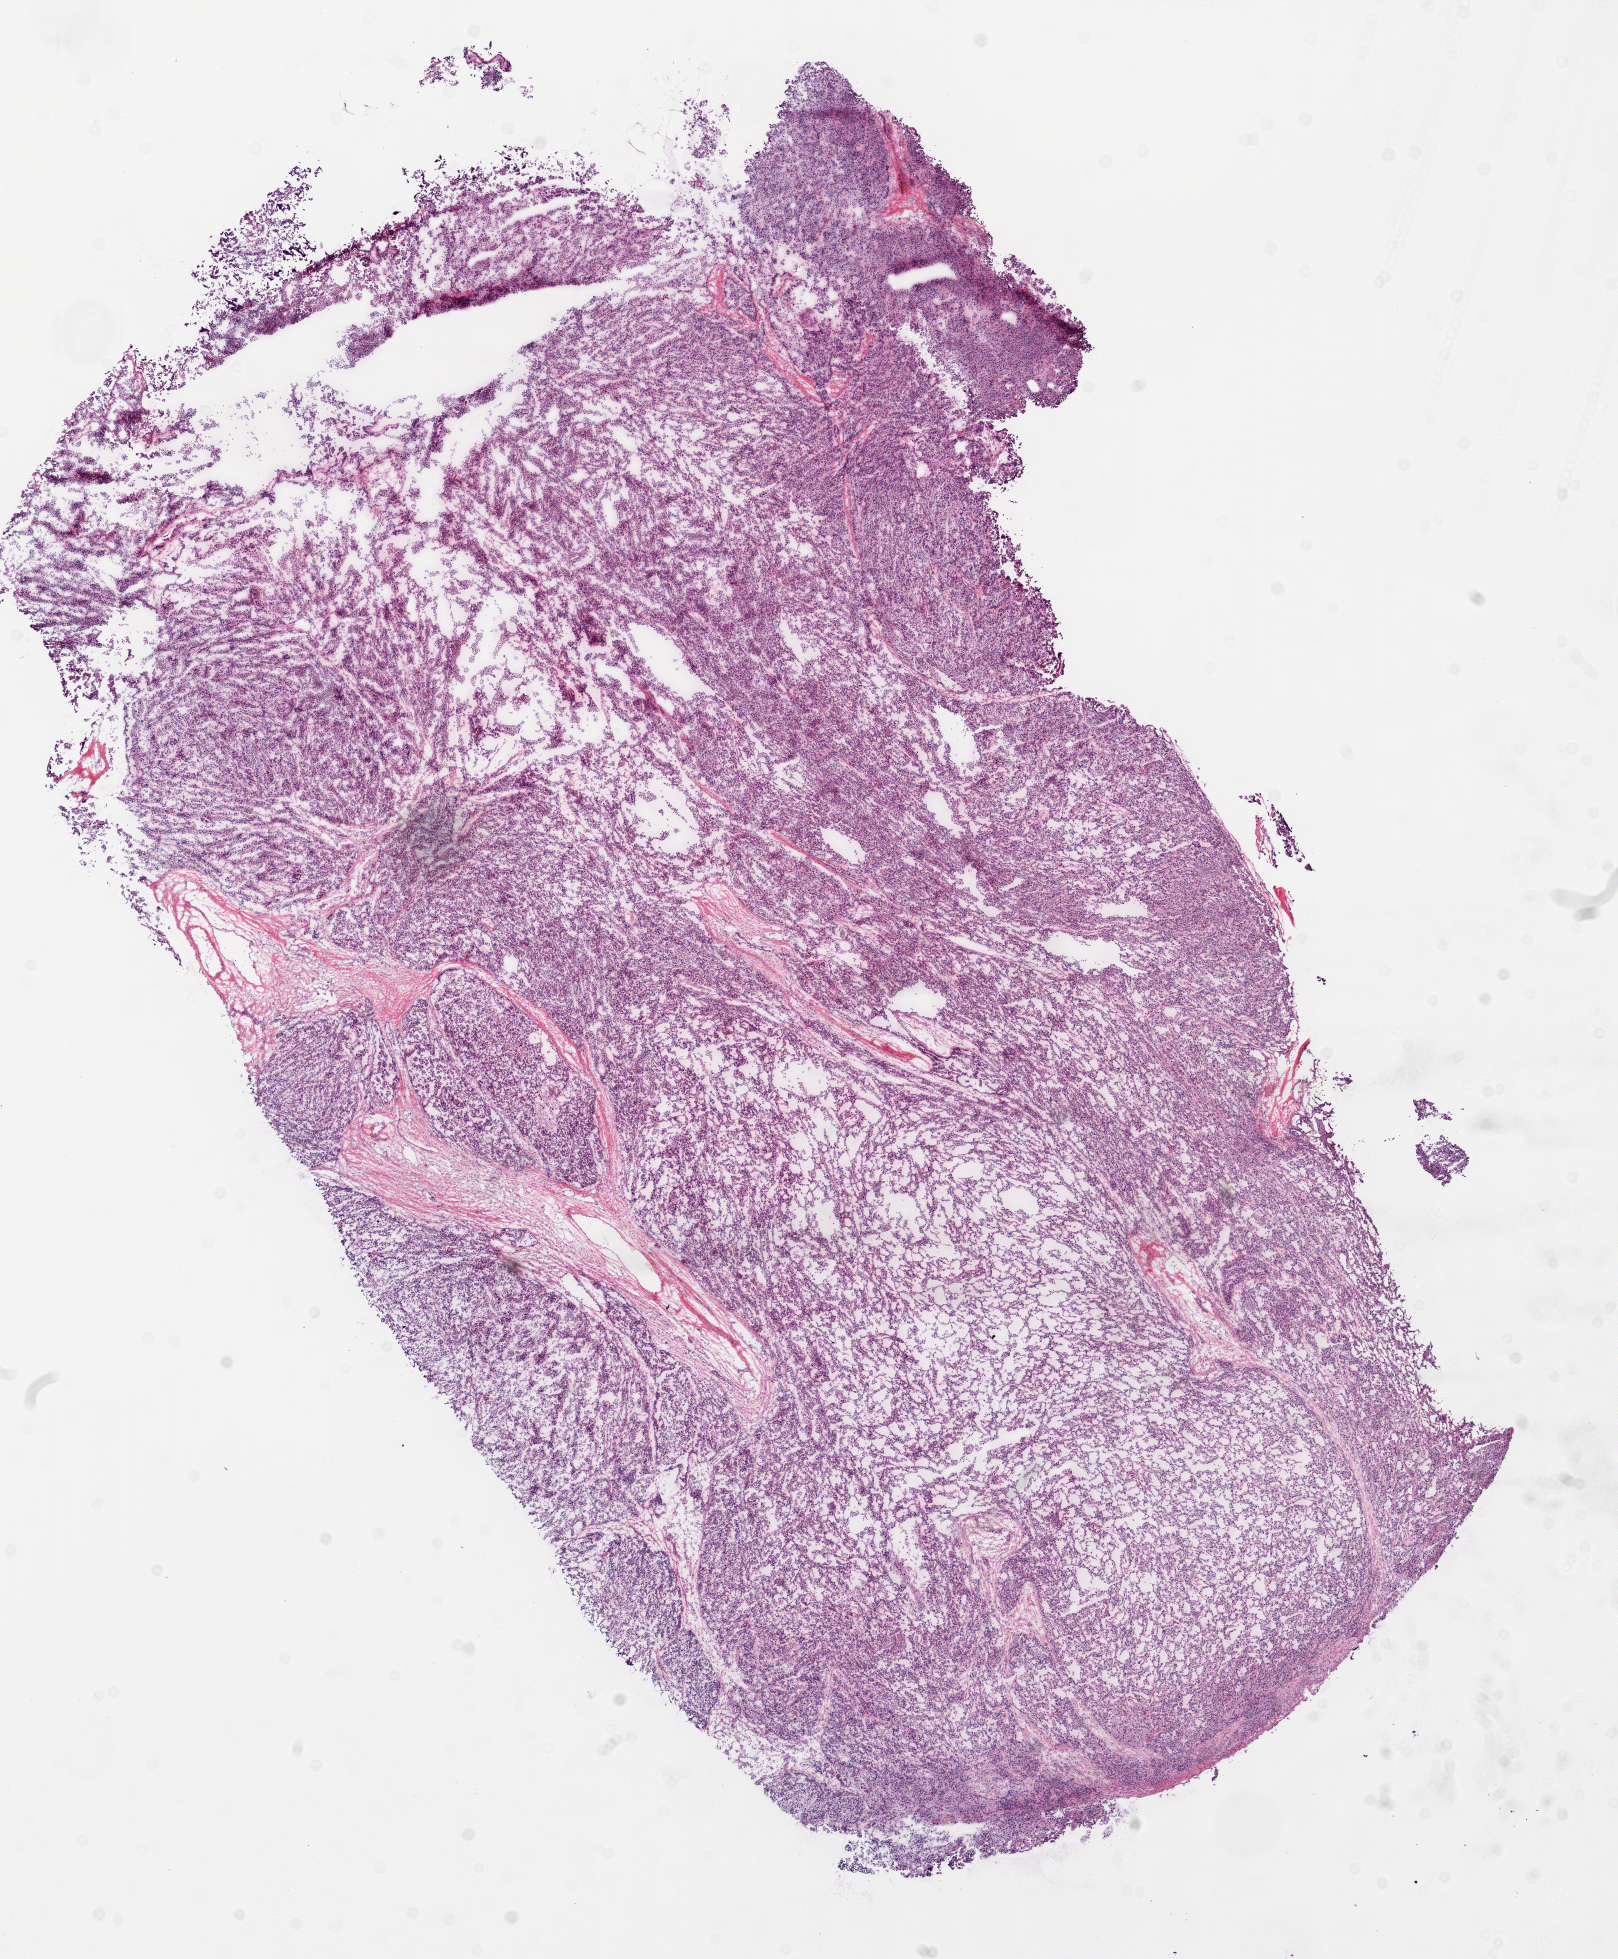
Whole-slide histology image, H&E-stained — shown as a low-resolution overview of the whole scanned area (about 13.0 x 15.8 mm, from a 20x scan), frozen section from the top of the tissue portion, ovary, primary tumour sample. Female, age 66 years at initial diagnosis.
Pathologic diagnosis: Serous cystadenocarcinoma, NOS.